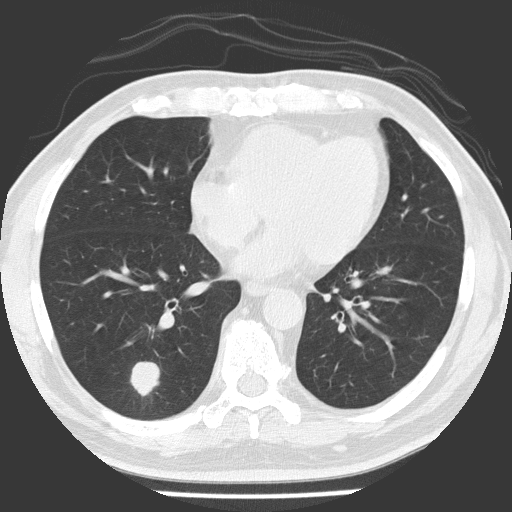
Axial slice from a low-dose chest CT screening exam; first (baseline) screen; lung window (W 1500 / L -600 HU); 2 mm slice thickness; slice 91 of 154 in the series; 512 × 512 image matrix. Male, age 56 years at enrolment. Former smoker at enrolment.
- Lesion marked by an expert reader, box from (x=113, y=349) to (x=167, y=404) px.
- Screening reader's record for this exam (one nodule recorded; not confirmed to be the boxed lesion): non-calcified nodule or mass ≥4 mm, right lower lobe, 21 × 17 mm, spiculated (stellate) margins, soft tissue attenuation.
- Official screen result: positive, change unspecified: nodule(s) >= 4 mm or enlarging nodule(s), mass(es), or other non-specific abnormalities suspicious for lung cancer.
- Participant outcome: lung cancer diagnosed 84 days after this screen — adenocarcinoma, NOS, right lower lobe, poorly differentiated (G3), stage IA (AJCC 6th edition), 24 mm at pathology.